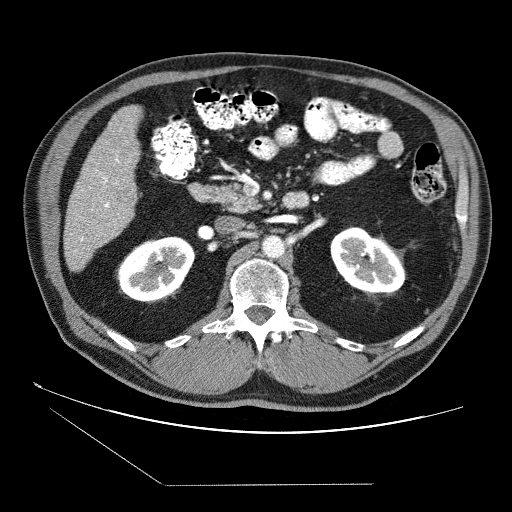
Contrast-enhanced abdominal CT (liver protocol), one axial slice; slice 21 of 87 in the series (ordered by position); 120 kVp; soft-tissue window (W 400 / L 40 HU); 2.5 mm slice thickness; 512 × 512 image matrix, field of view 400 × 400 mm. From the clinical record (not read from this slice): diagnosis: hepatocellular carcinoma (patient treated with transarterial chemoembolisation; whether this scan precedes or follows treatment is not stated here); TNM stage (as recorded): Stage-II; Child-Pugh class: B; tumour differentiation: no biopsy; tumour nodularity: multinodular.
Structures marked on this image (semi-automatically segmented with operator editing):
- liver parenchyma outside the tumour (the mass and vessels are separate outlines, so this box may not span the whole liver): box from (x=64, y=106) to (x=140, y=272) px
- liver vessels: (x=70, y=157)–(x=119, y=252)